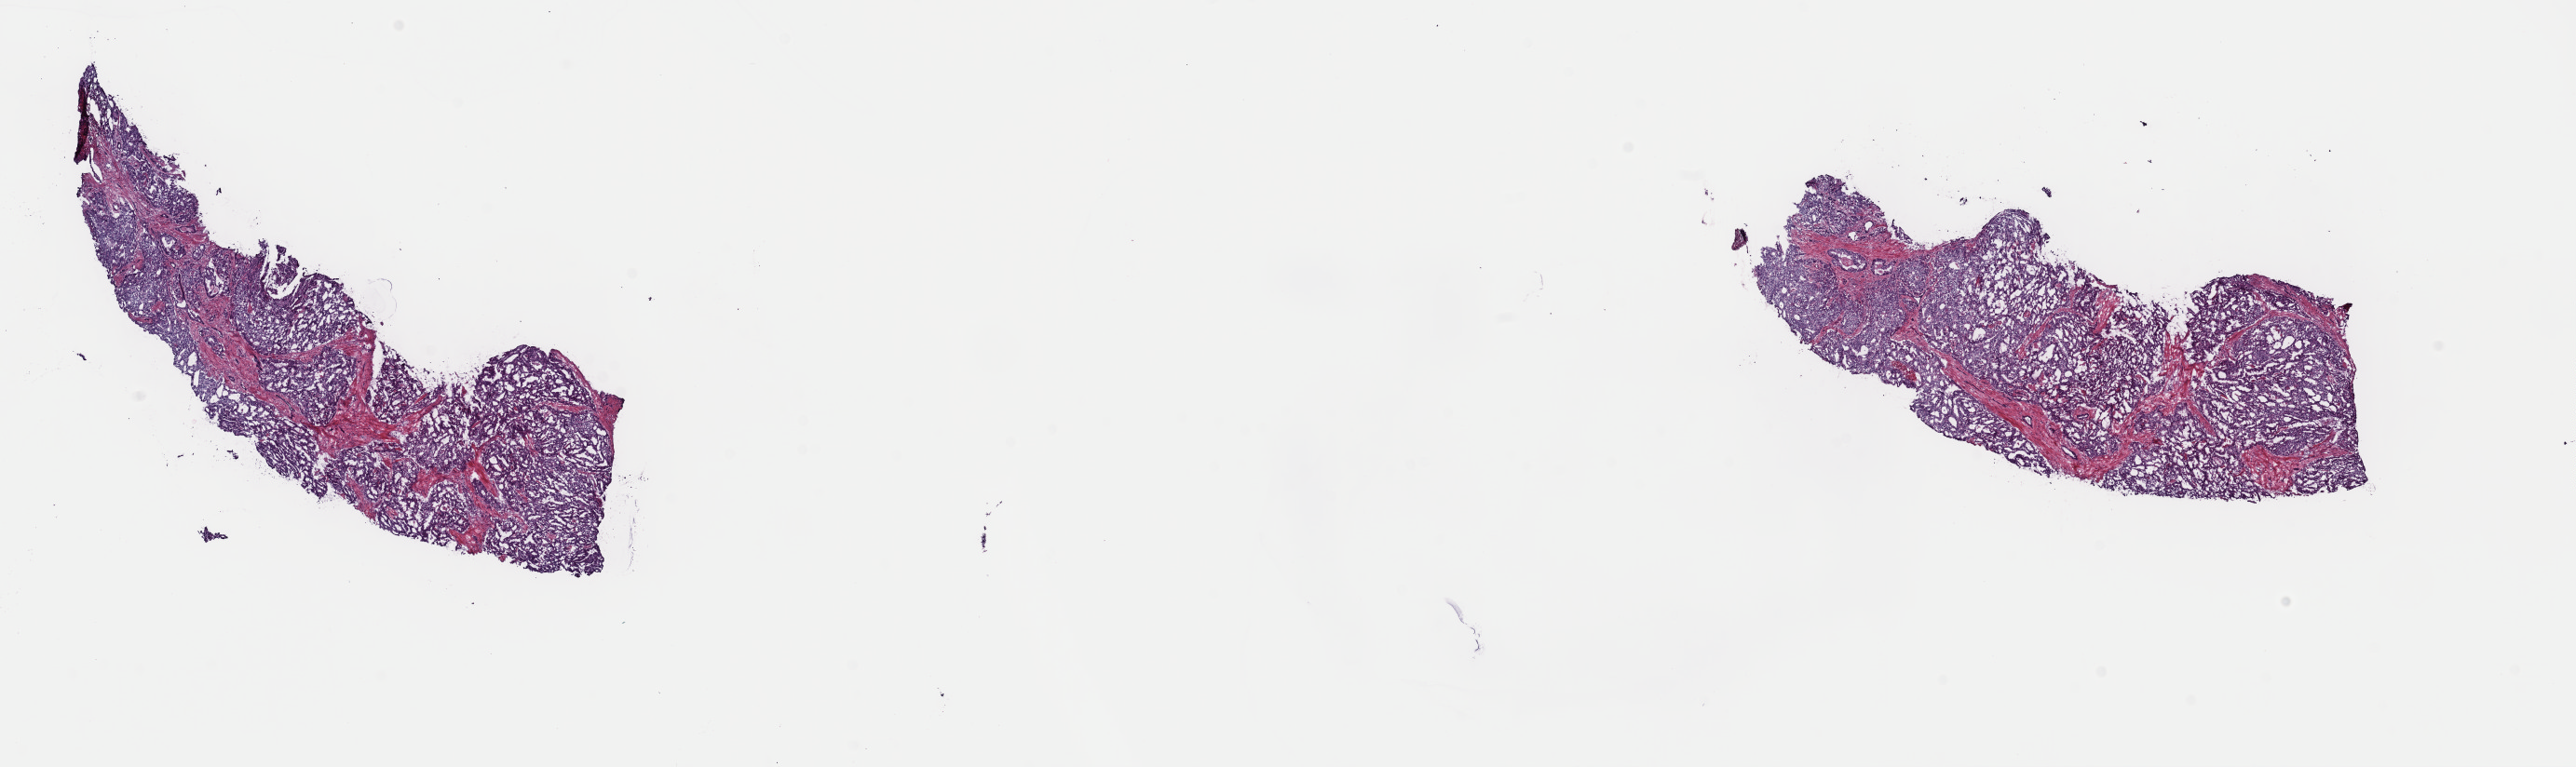
Hematoxylin and eosin (H&E) stained whole-slide image — shown as a low-resolution overview of the whole scanned area (about 21.9 x 6.5 mm, from a 40x scan), frozen section from the top of the tissue portion, prostate, primary tumour sample. Male, age 71 years at initial diagnosis. Gleason score: 9 (4+5). Slide review estimates, as recorded: tumour cells 100%, tumour nuclei 95%, normal cells 0%, stromal cells 0%, necrosis 0%. Inflammatory infiltration, as recorded: lymphocyte infiltration 0%, monocyte infiltration 0%, neutrophil infiltration 0%.
- laterality: bilateral
- diagnosis: Infiltrating duct carcinoma, NOS